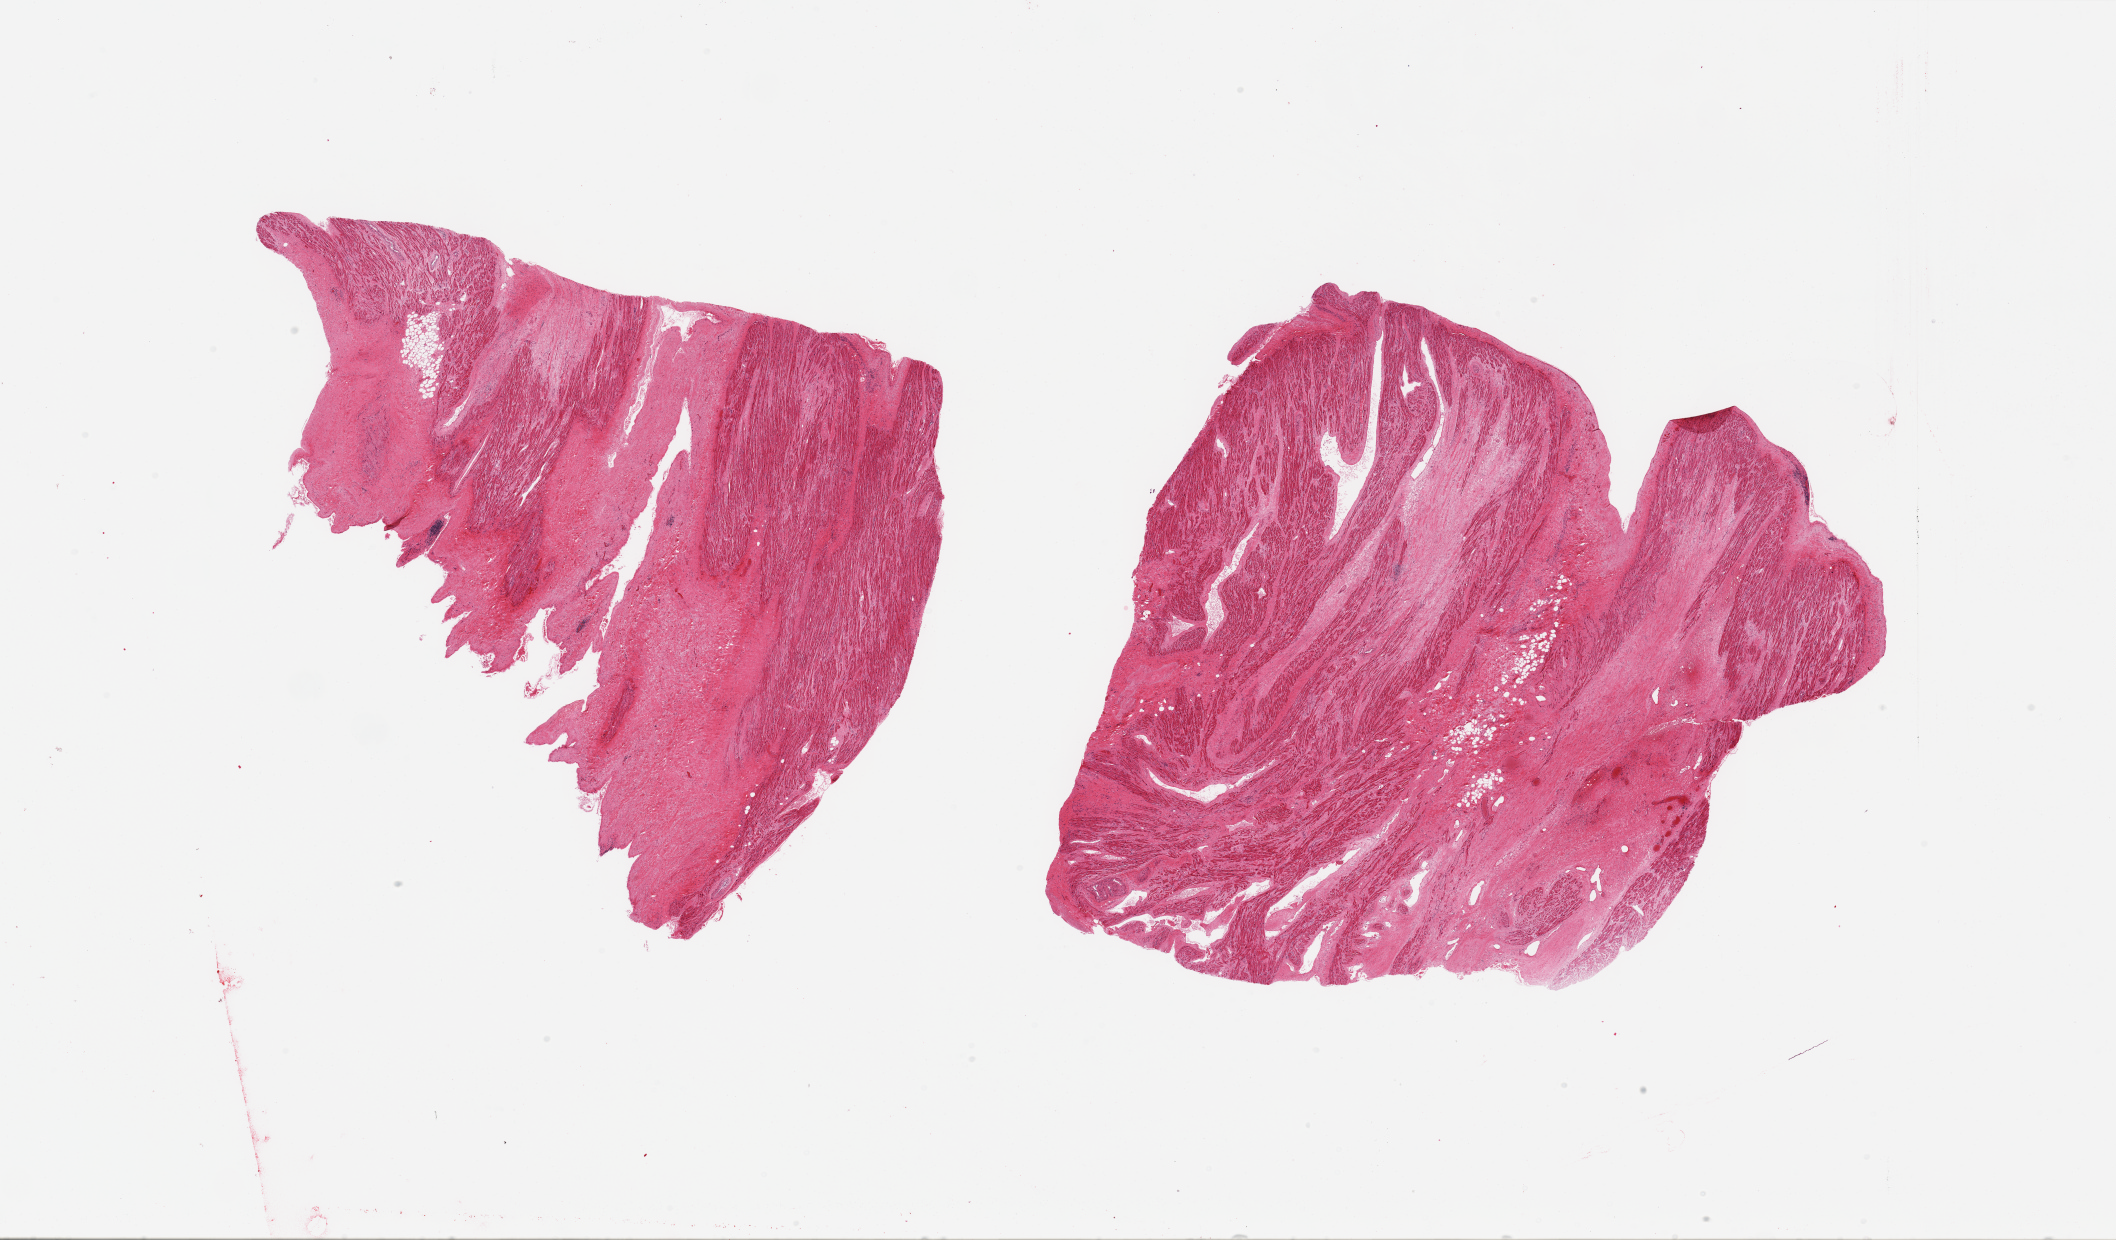
Whole-slide image, hematoxylin and eosin (H&E) stain — low-resolution overview of the scanned area, about 33.5 x 19.6 mm, PAXgene-fixed, paraffin-embedded tissue, sampled site (target tissue): auricular appendage, donor tissue sample. Male donor.
Reviewer comment on this tissue sample: 2 pieces; muscle and fibrous tissue about equally represented.